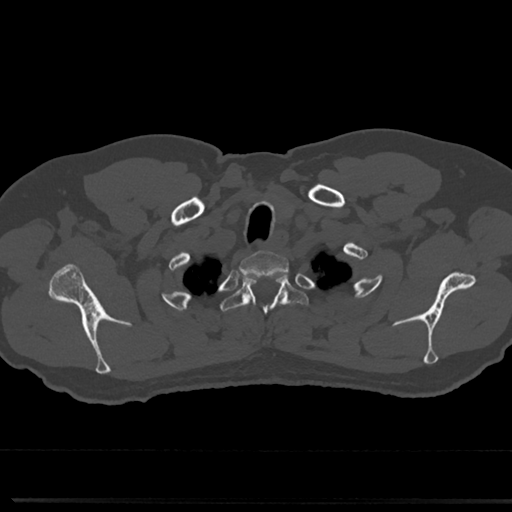
CT including the spine, one axial slice; position 646 of 817 along the scan axis; reconstruction kernel Br40s/3; 120 kVp; bone window (W 1800 / L 400 HU); 0.5 mm slice thickness; 512 × 512 image matrix, field of view 355 × 355 mm. Male patient, age 61 years. Case-level facts recorded for this patient, not image findings: primary cancer: prostate.
Outlined on this slice (semi-automatically segmented with operator editing):
- T1 vertebra: bounding box (x1, y1, x2, y2) in pixels: (243, 252, 286, 266)
- T2 vertebra: (226, 273, 304, 328)